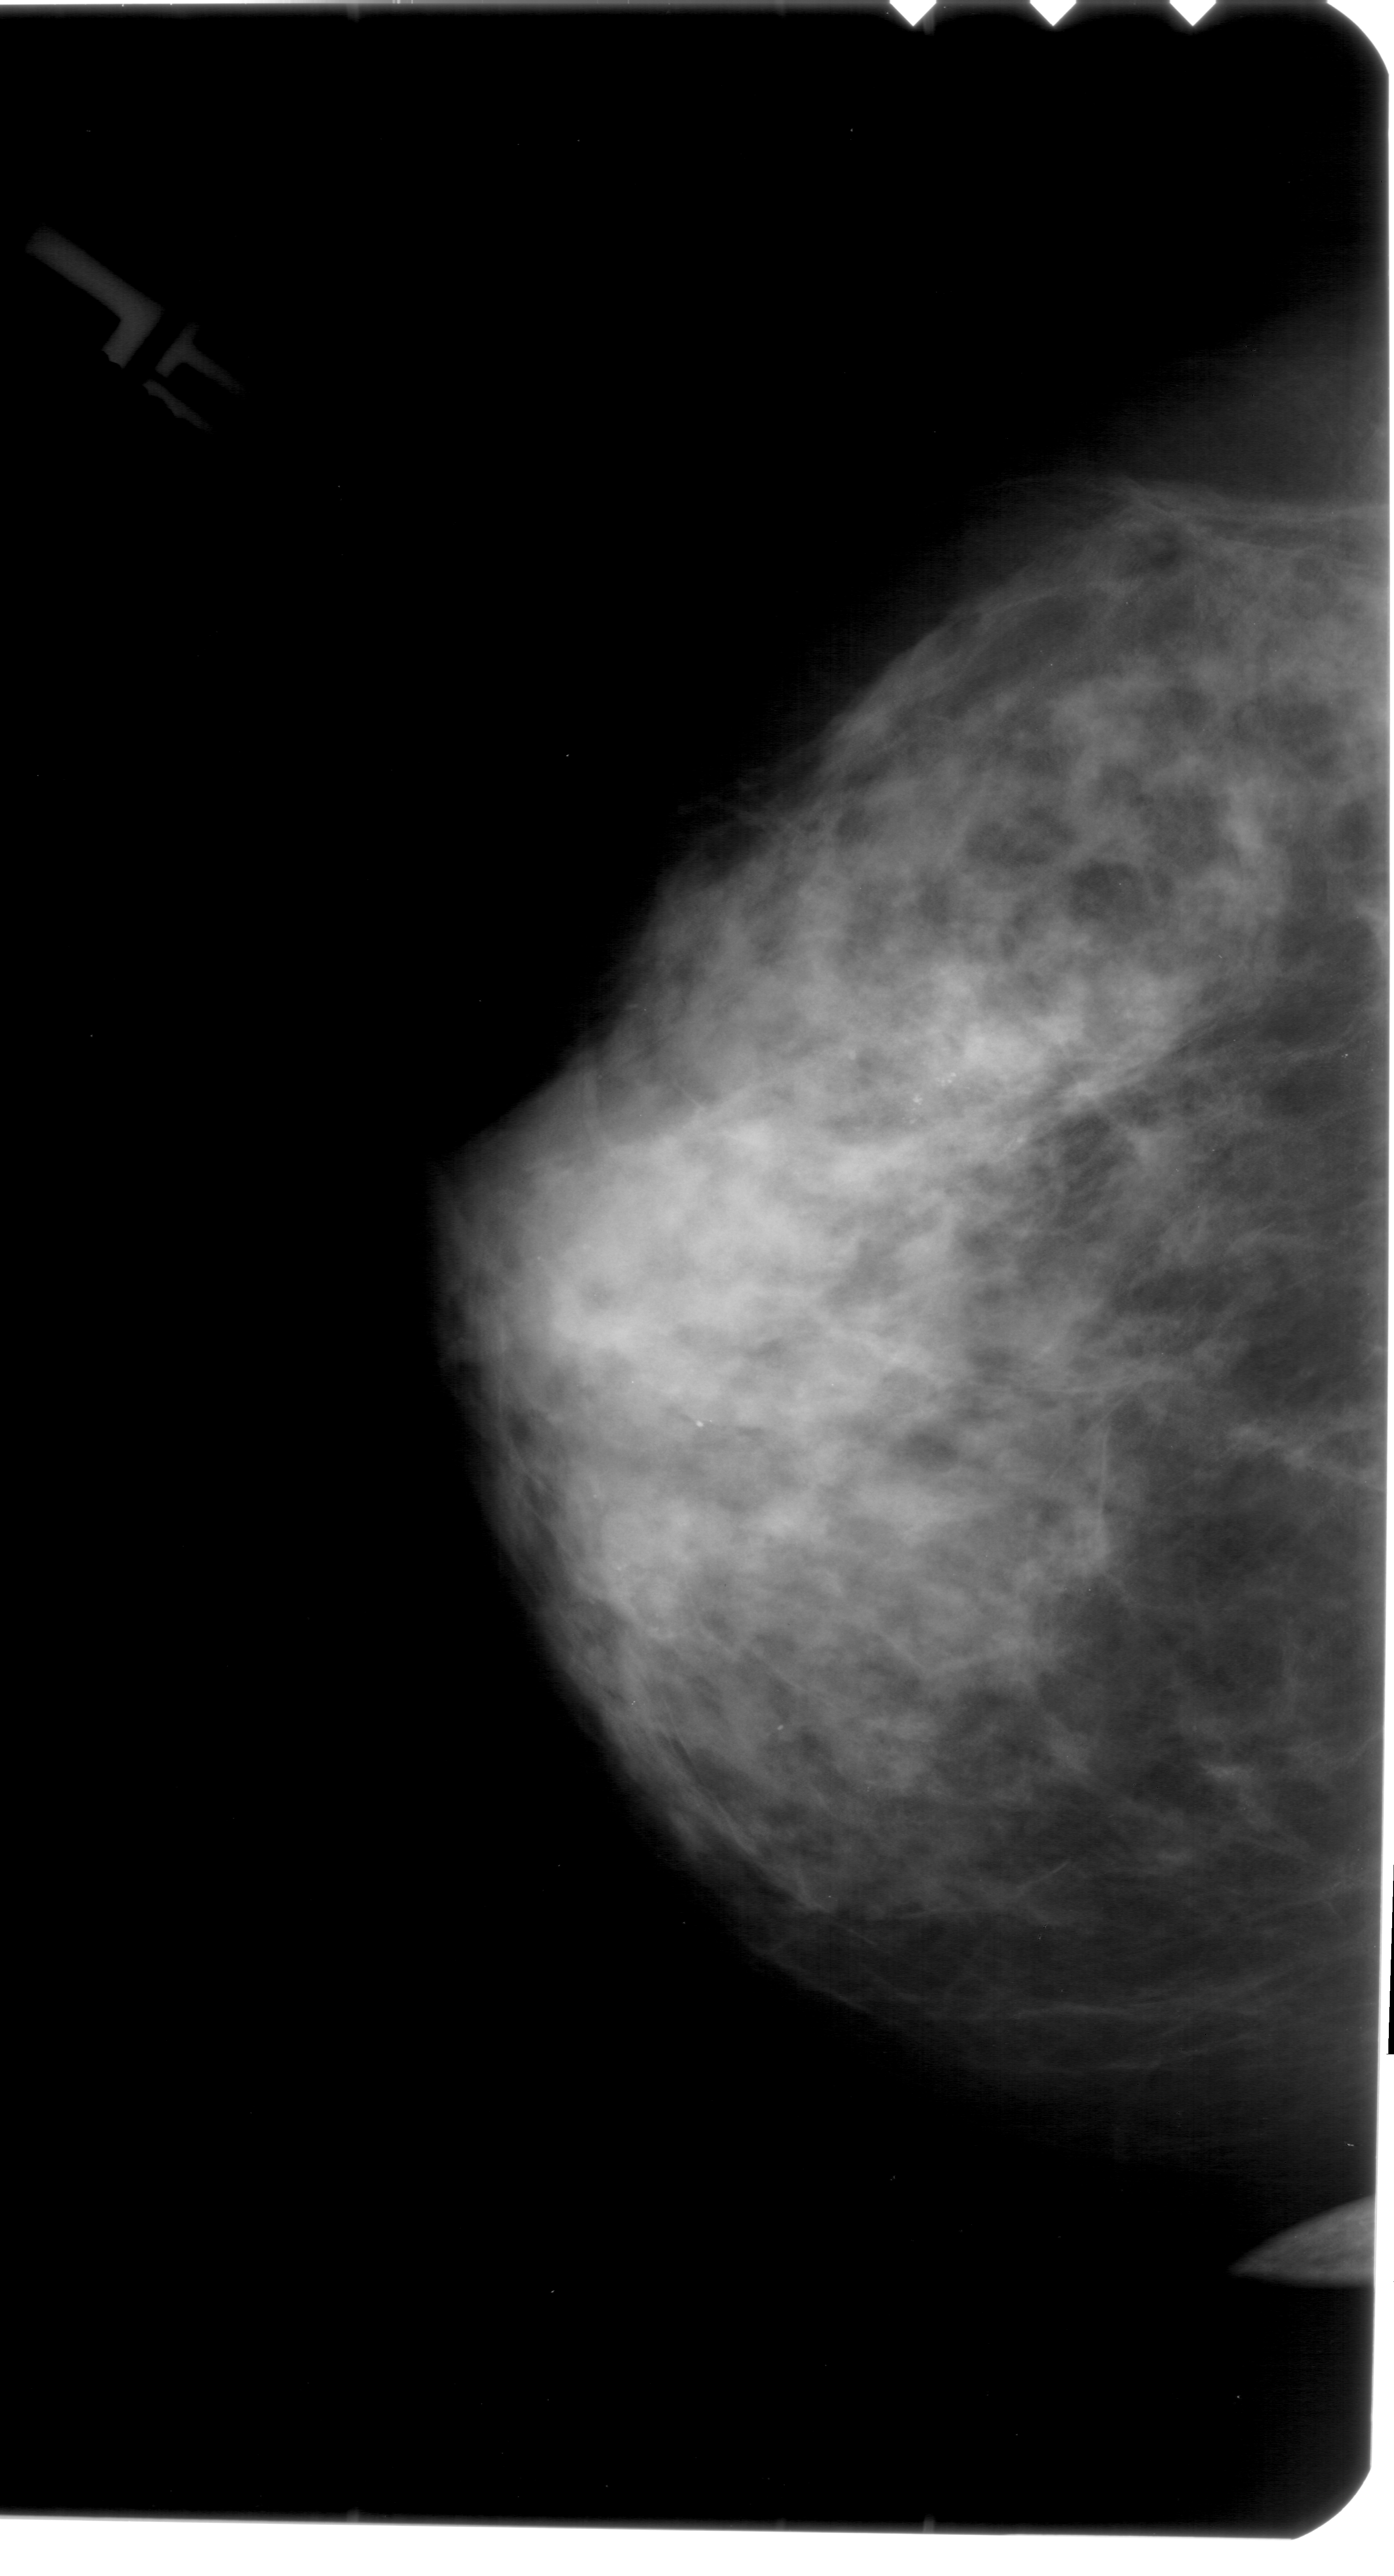
Mammogram (digitized film), left breast, CC view, breast composition: extremely dense (BI-RADS density category 4 of 4).
- Finding: calcifications, morphology pleomorphic, distribution clustered; BI-RADS assessment category 4; subtlety rating 4 on a 1 (subtle) to 5 (obvious) scale; pathology (as recorded): malignant.